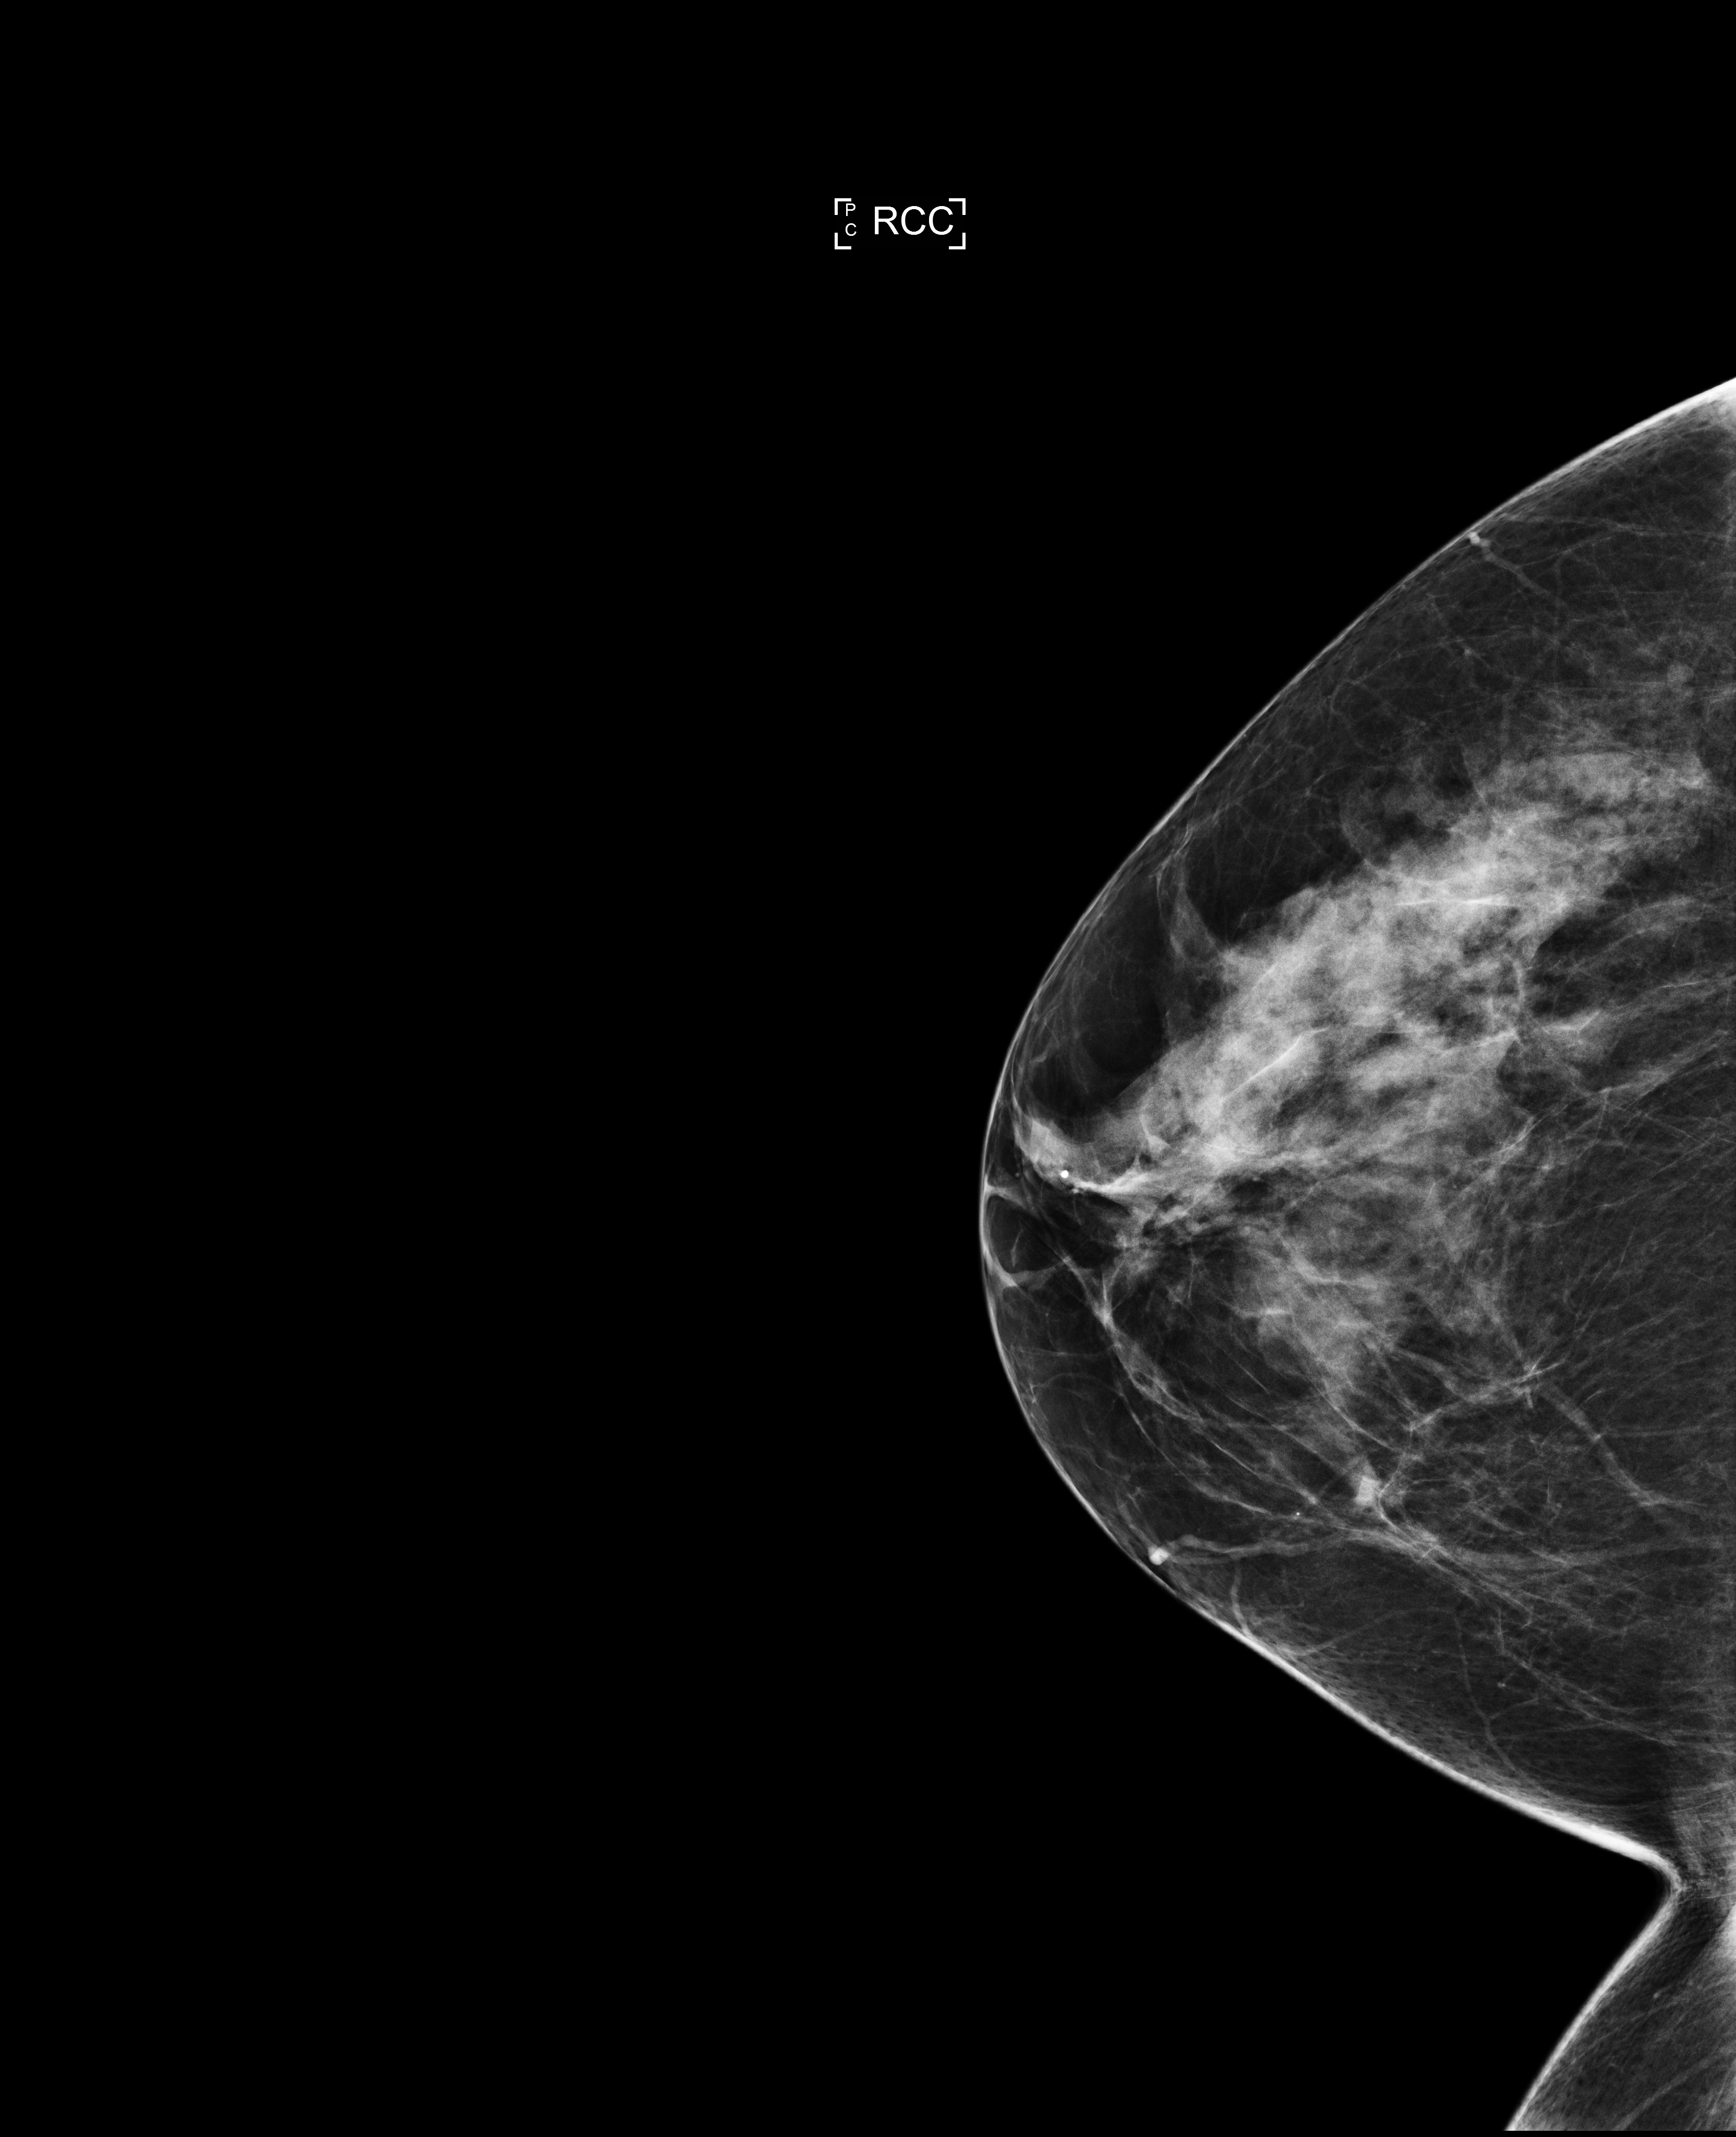
Screening examination. Patient: female, 49 years.
Image type: full-field digital mammogram. Breast: right. Projection: cranio-caudal projection.